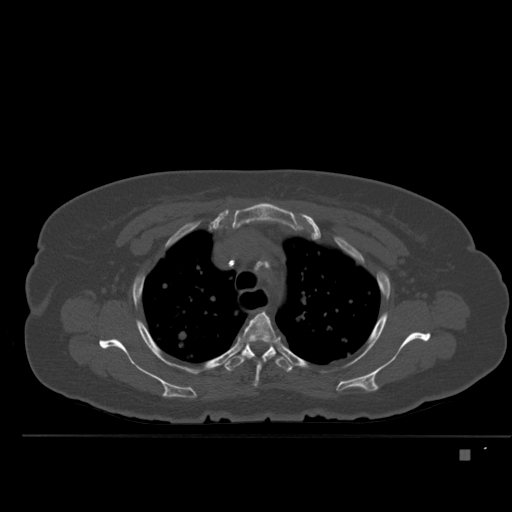
CT including the spine, one axial slice. Slice 374 of 477 in the series (ordered by position). Bone window (W 1800 / L 400 HU). 1.5 mm slice thickness. 512 × 512 image matrix, field of view 422 × 422 mm. Female patient, age 74 years. Case-level facts recorded for this patient, not image findings: primary cancer: colon.
Structures marked on this image (semi-automatic segmentation, software-assisted and operator-edited):
- T3 vertebra: bounding box <240,311,278,387> (left, top, right, bottom; pixels)
- T4 vertebra: <225,344,293,372>